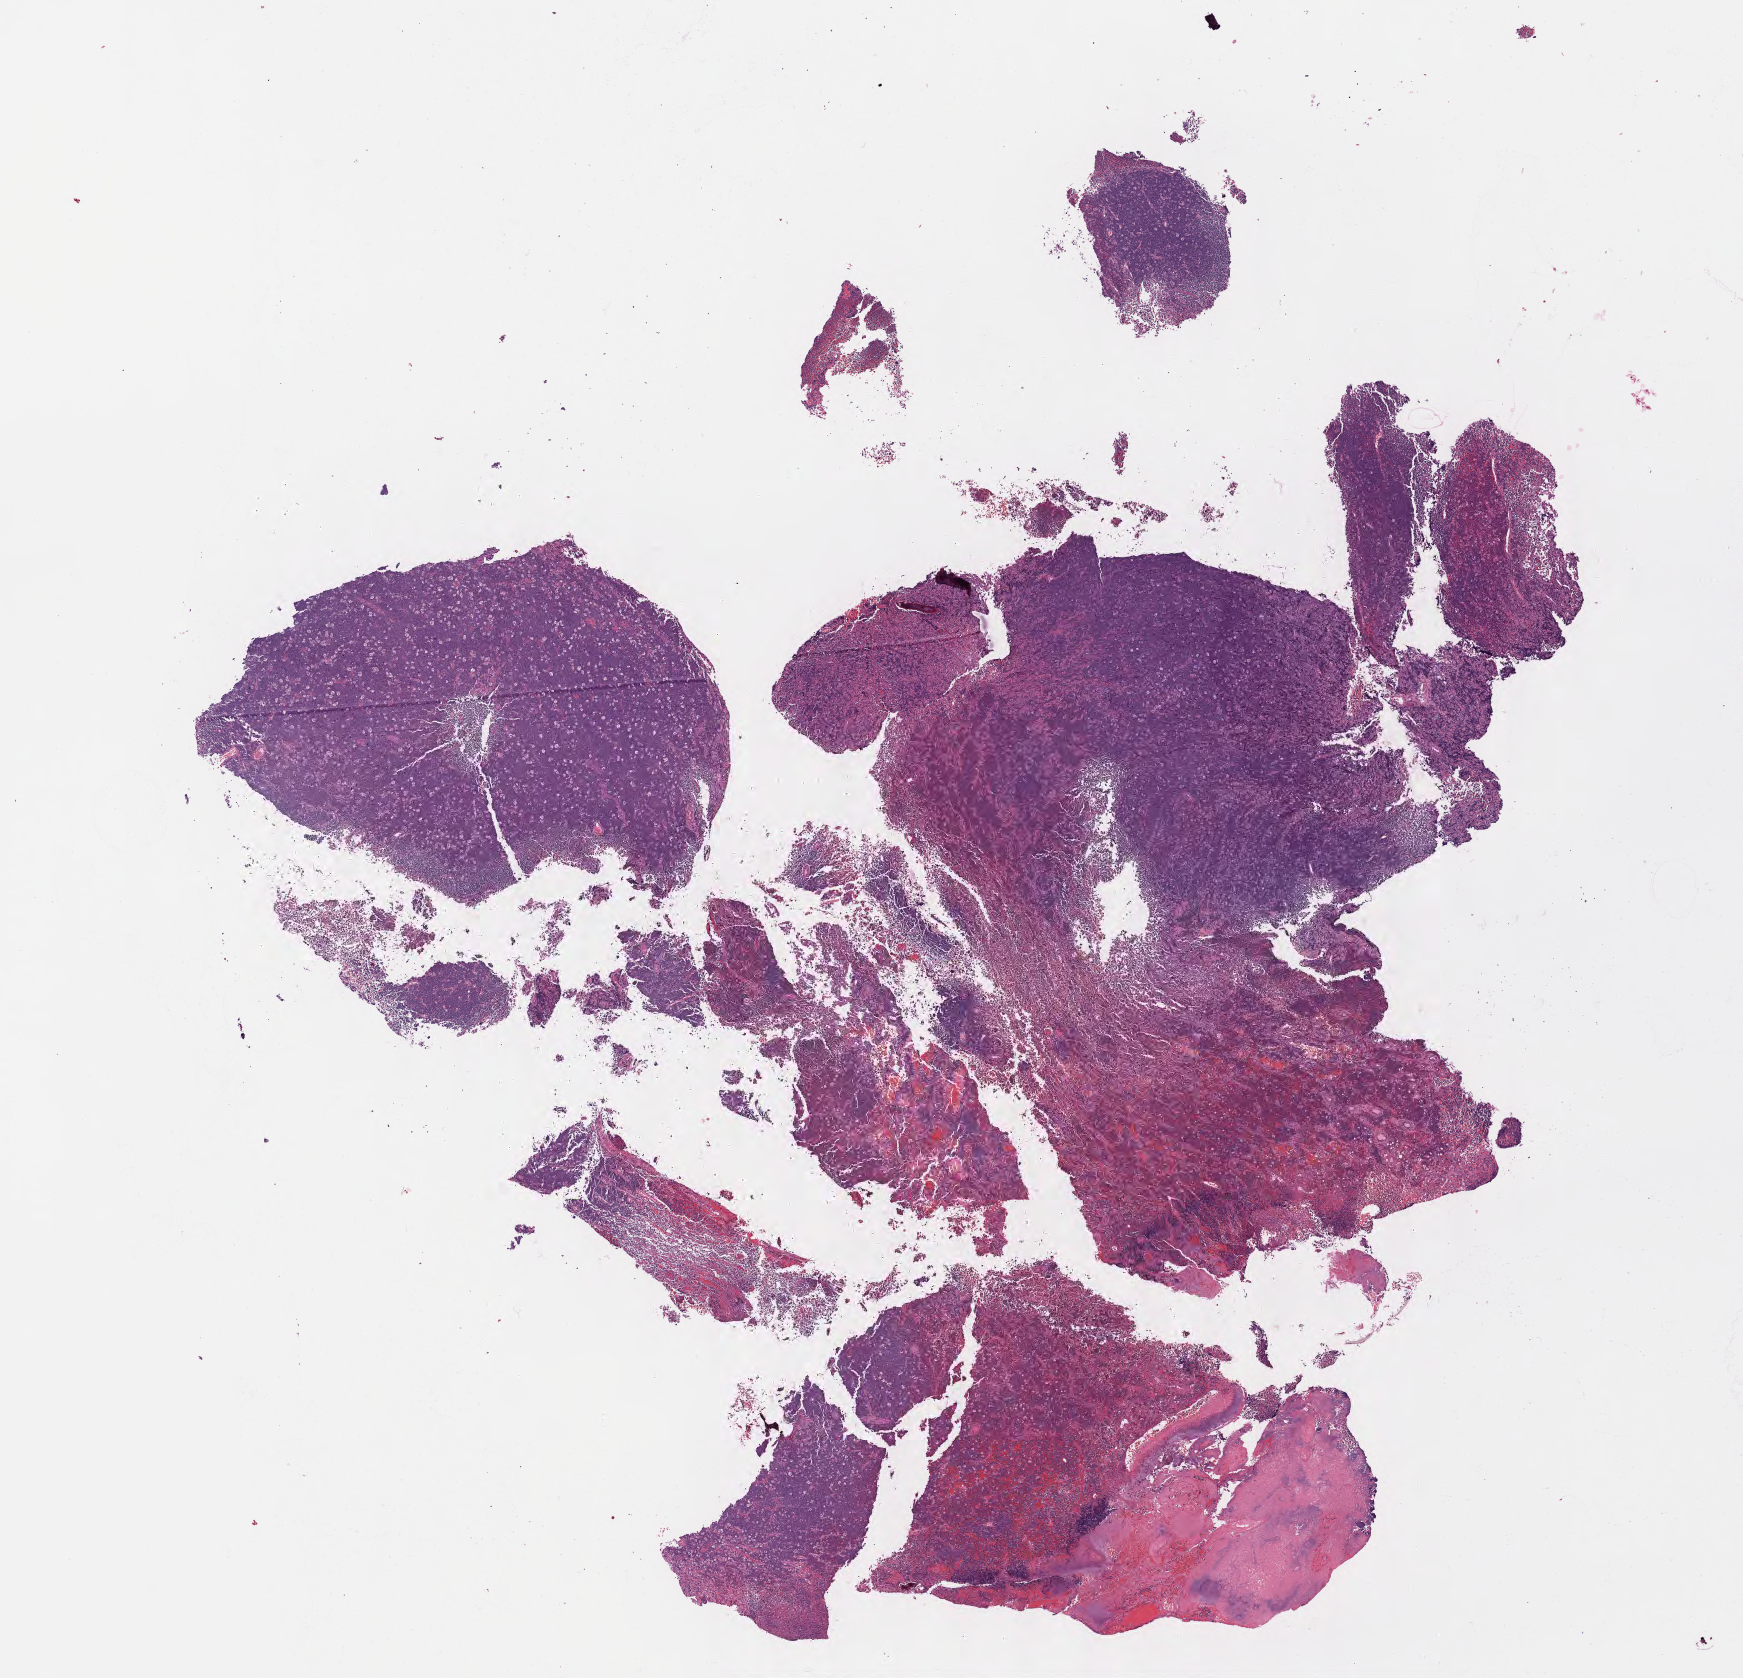
Whole-slide image, haematoxylin and eosin stain, low-resolution overview of the scanned area, about 14.1 x 13.6 mm; formalin-fixed, paraffin-embedded (FFPE) tissue; primary tumor; site: cranium. Female, age 5 years at initial diagnosis.
Histologic diagnosis: Burkitt lymphoma, NOS.